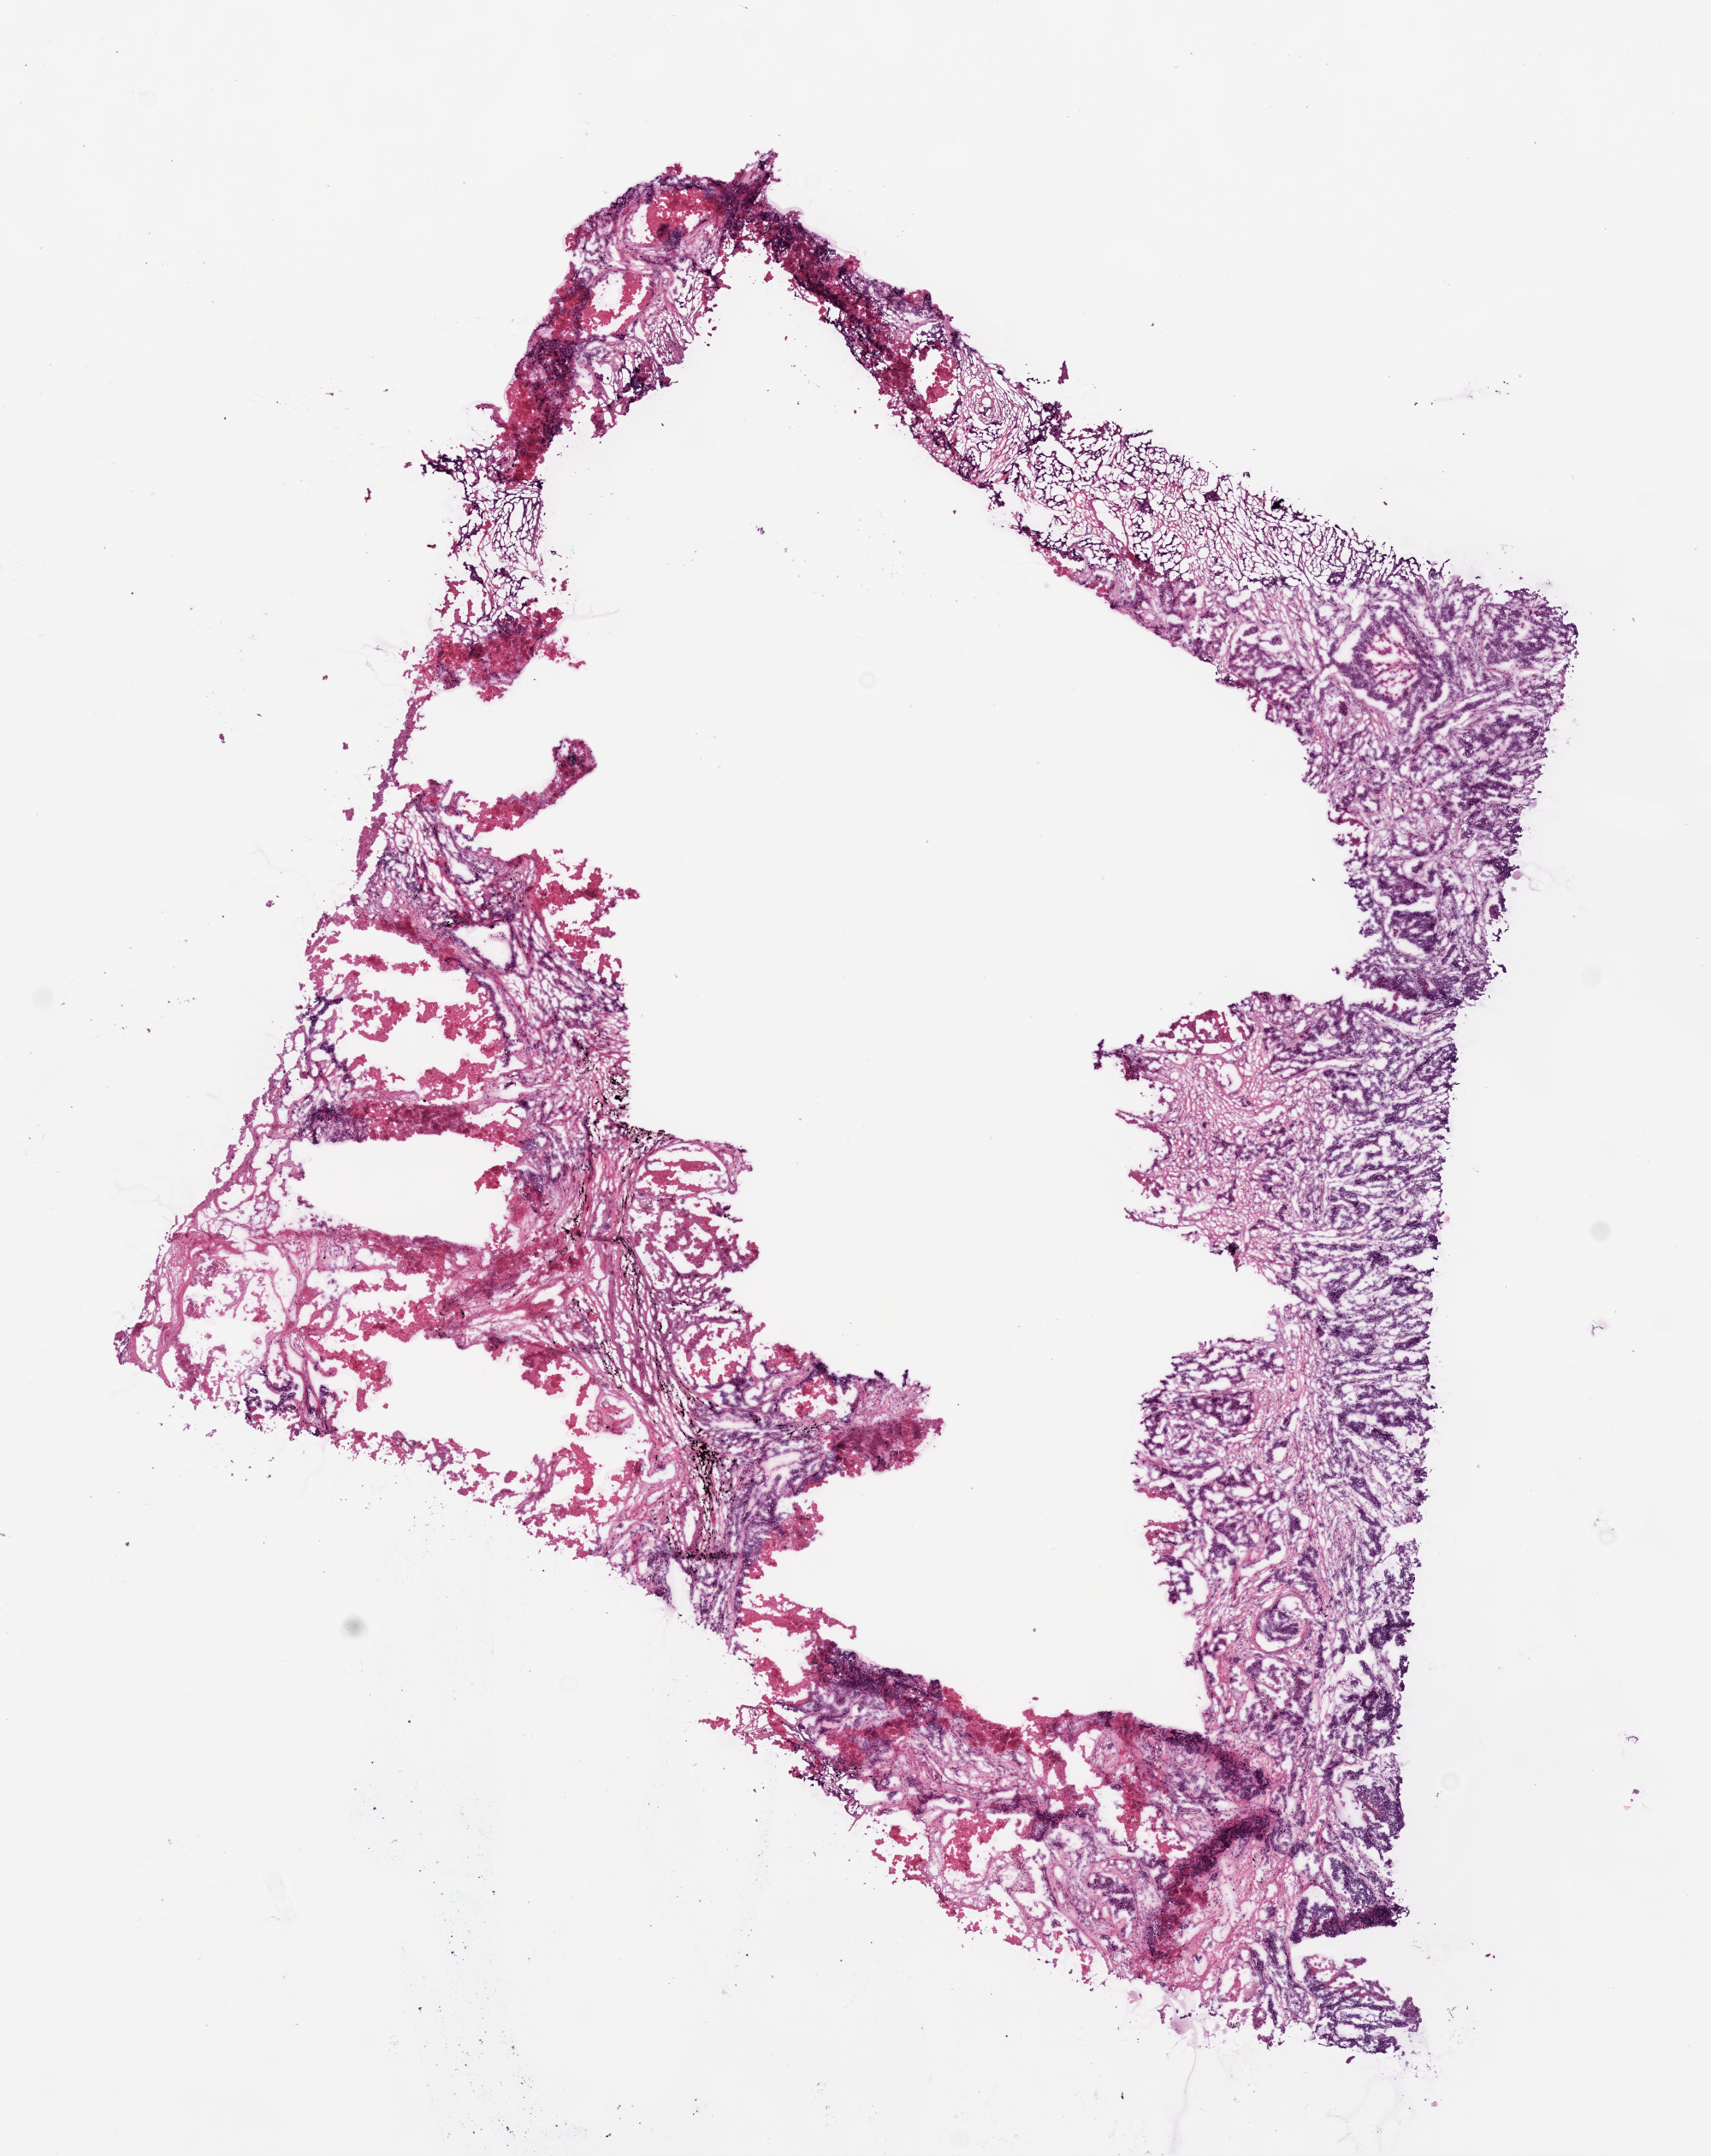
H&E-stained whole-slide image, low-resolution overview of the scanned area, about 8.0 x 10.1 mm (acquisition: 20x scan), frozen section from the bottom of the tissue portion, primary tumour sample from the lung. Patient: female, age at initial diagnosis 70 years. Slide review estimates, as recorded: tumour cells 35%, tumour nuclei 80%, normal cells 0%, stromal cells 45%, necrosis 20%.
Diagnosis: Adenocarcinoma, NOS.